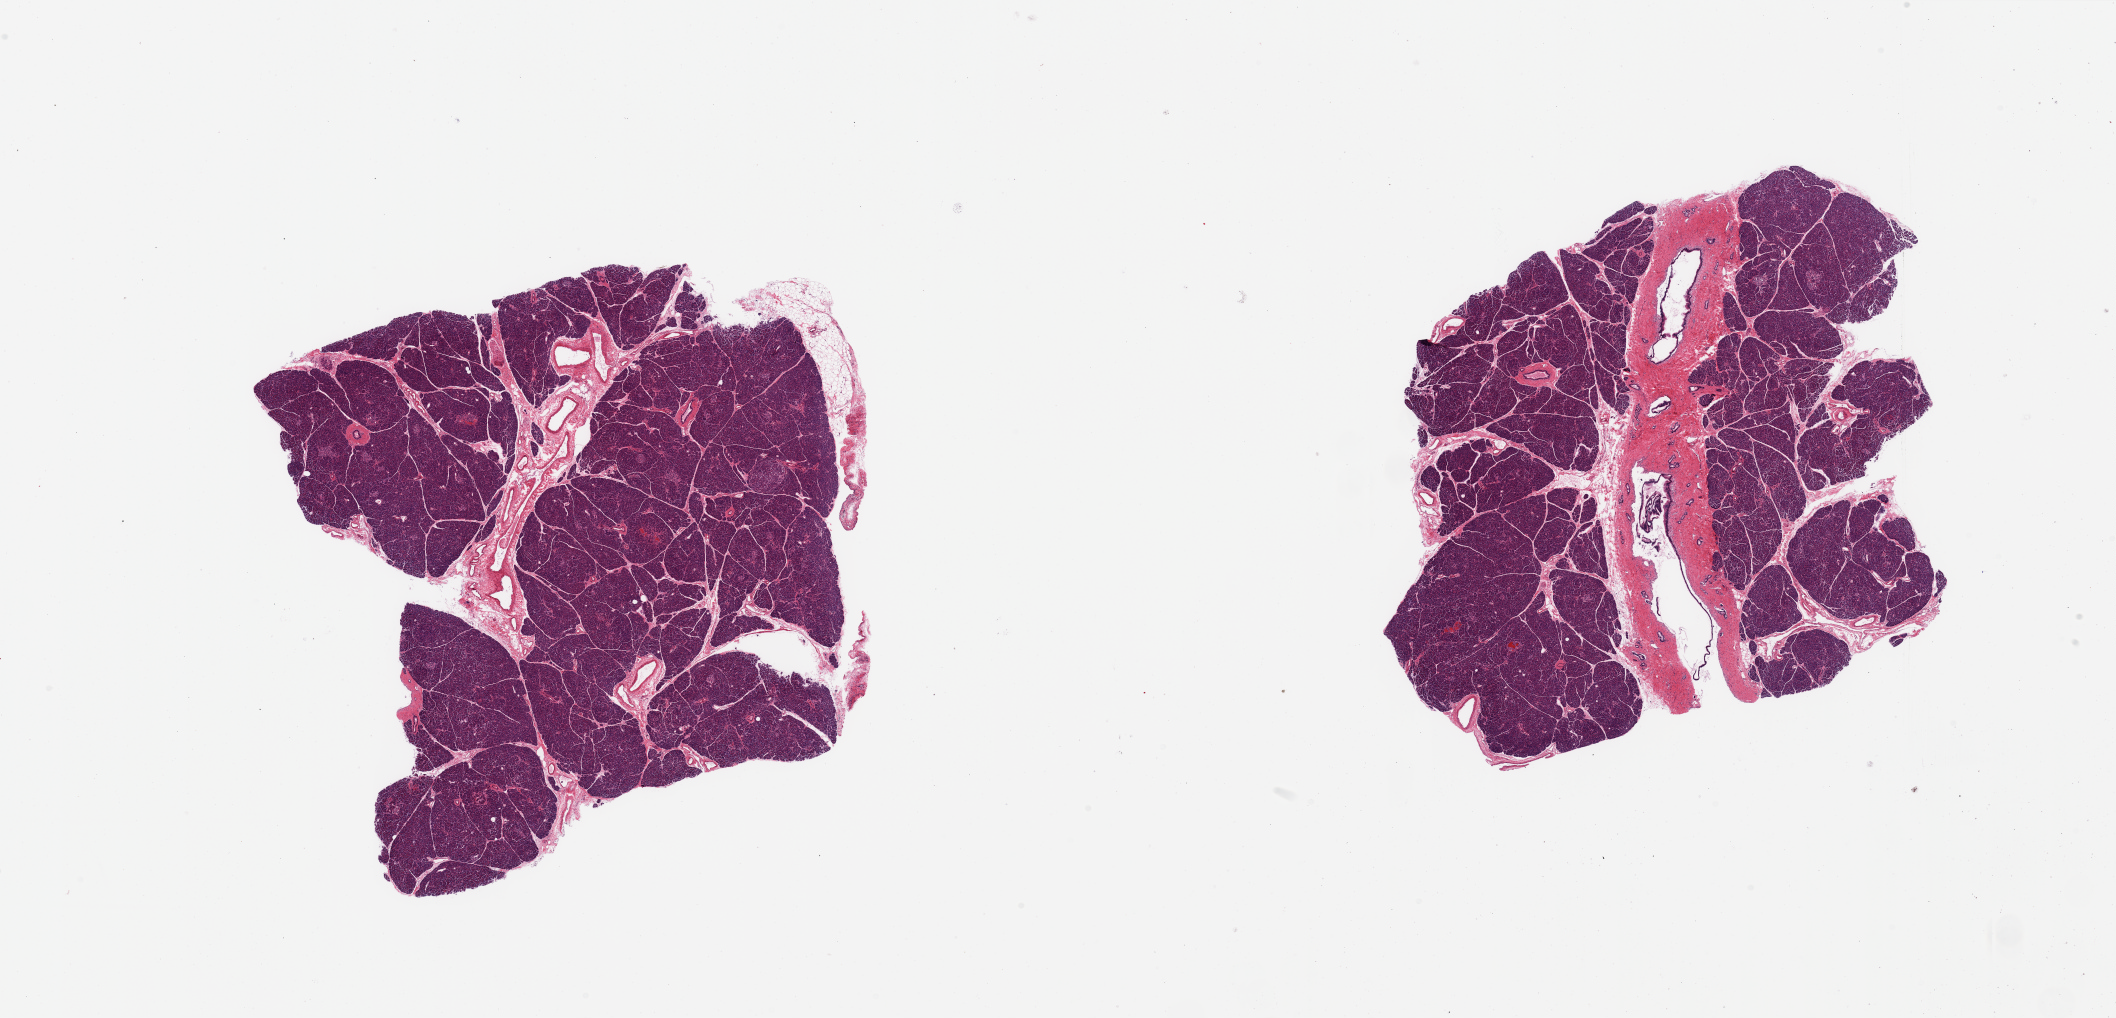
Hematoxylin and eosin (H&E) whole-slide image, brightfield, whole scanned area (about 33.5 x 16.1 mm, slide scanned at 20x) shown as a low-resolution overview, PAXgene-fixed paraffin-embedded (PFPE) section, target tissue: pancreas, tissue donor sample. Donor: male.
Reviewer comment on this tissue sample: 2 pieces; large duct located at center of 1 piece; prominent blood vessels at center of other piece.